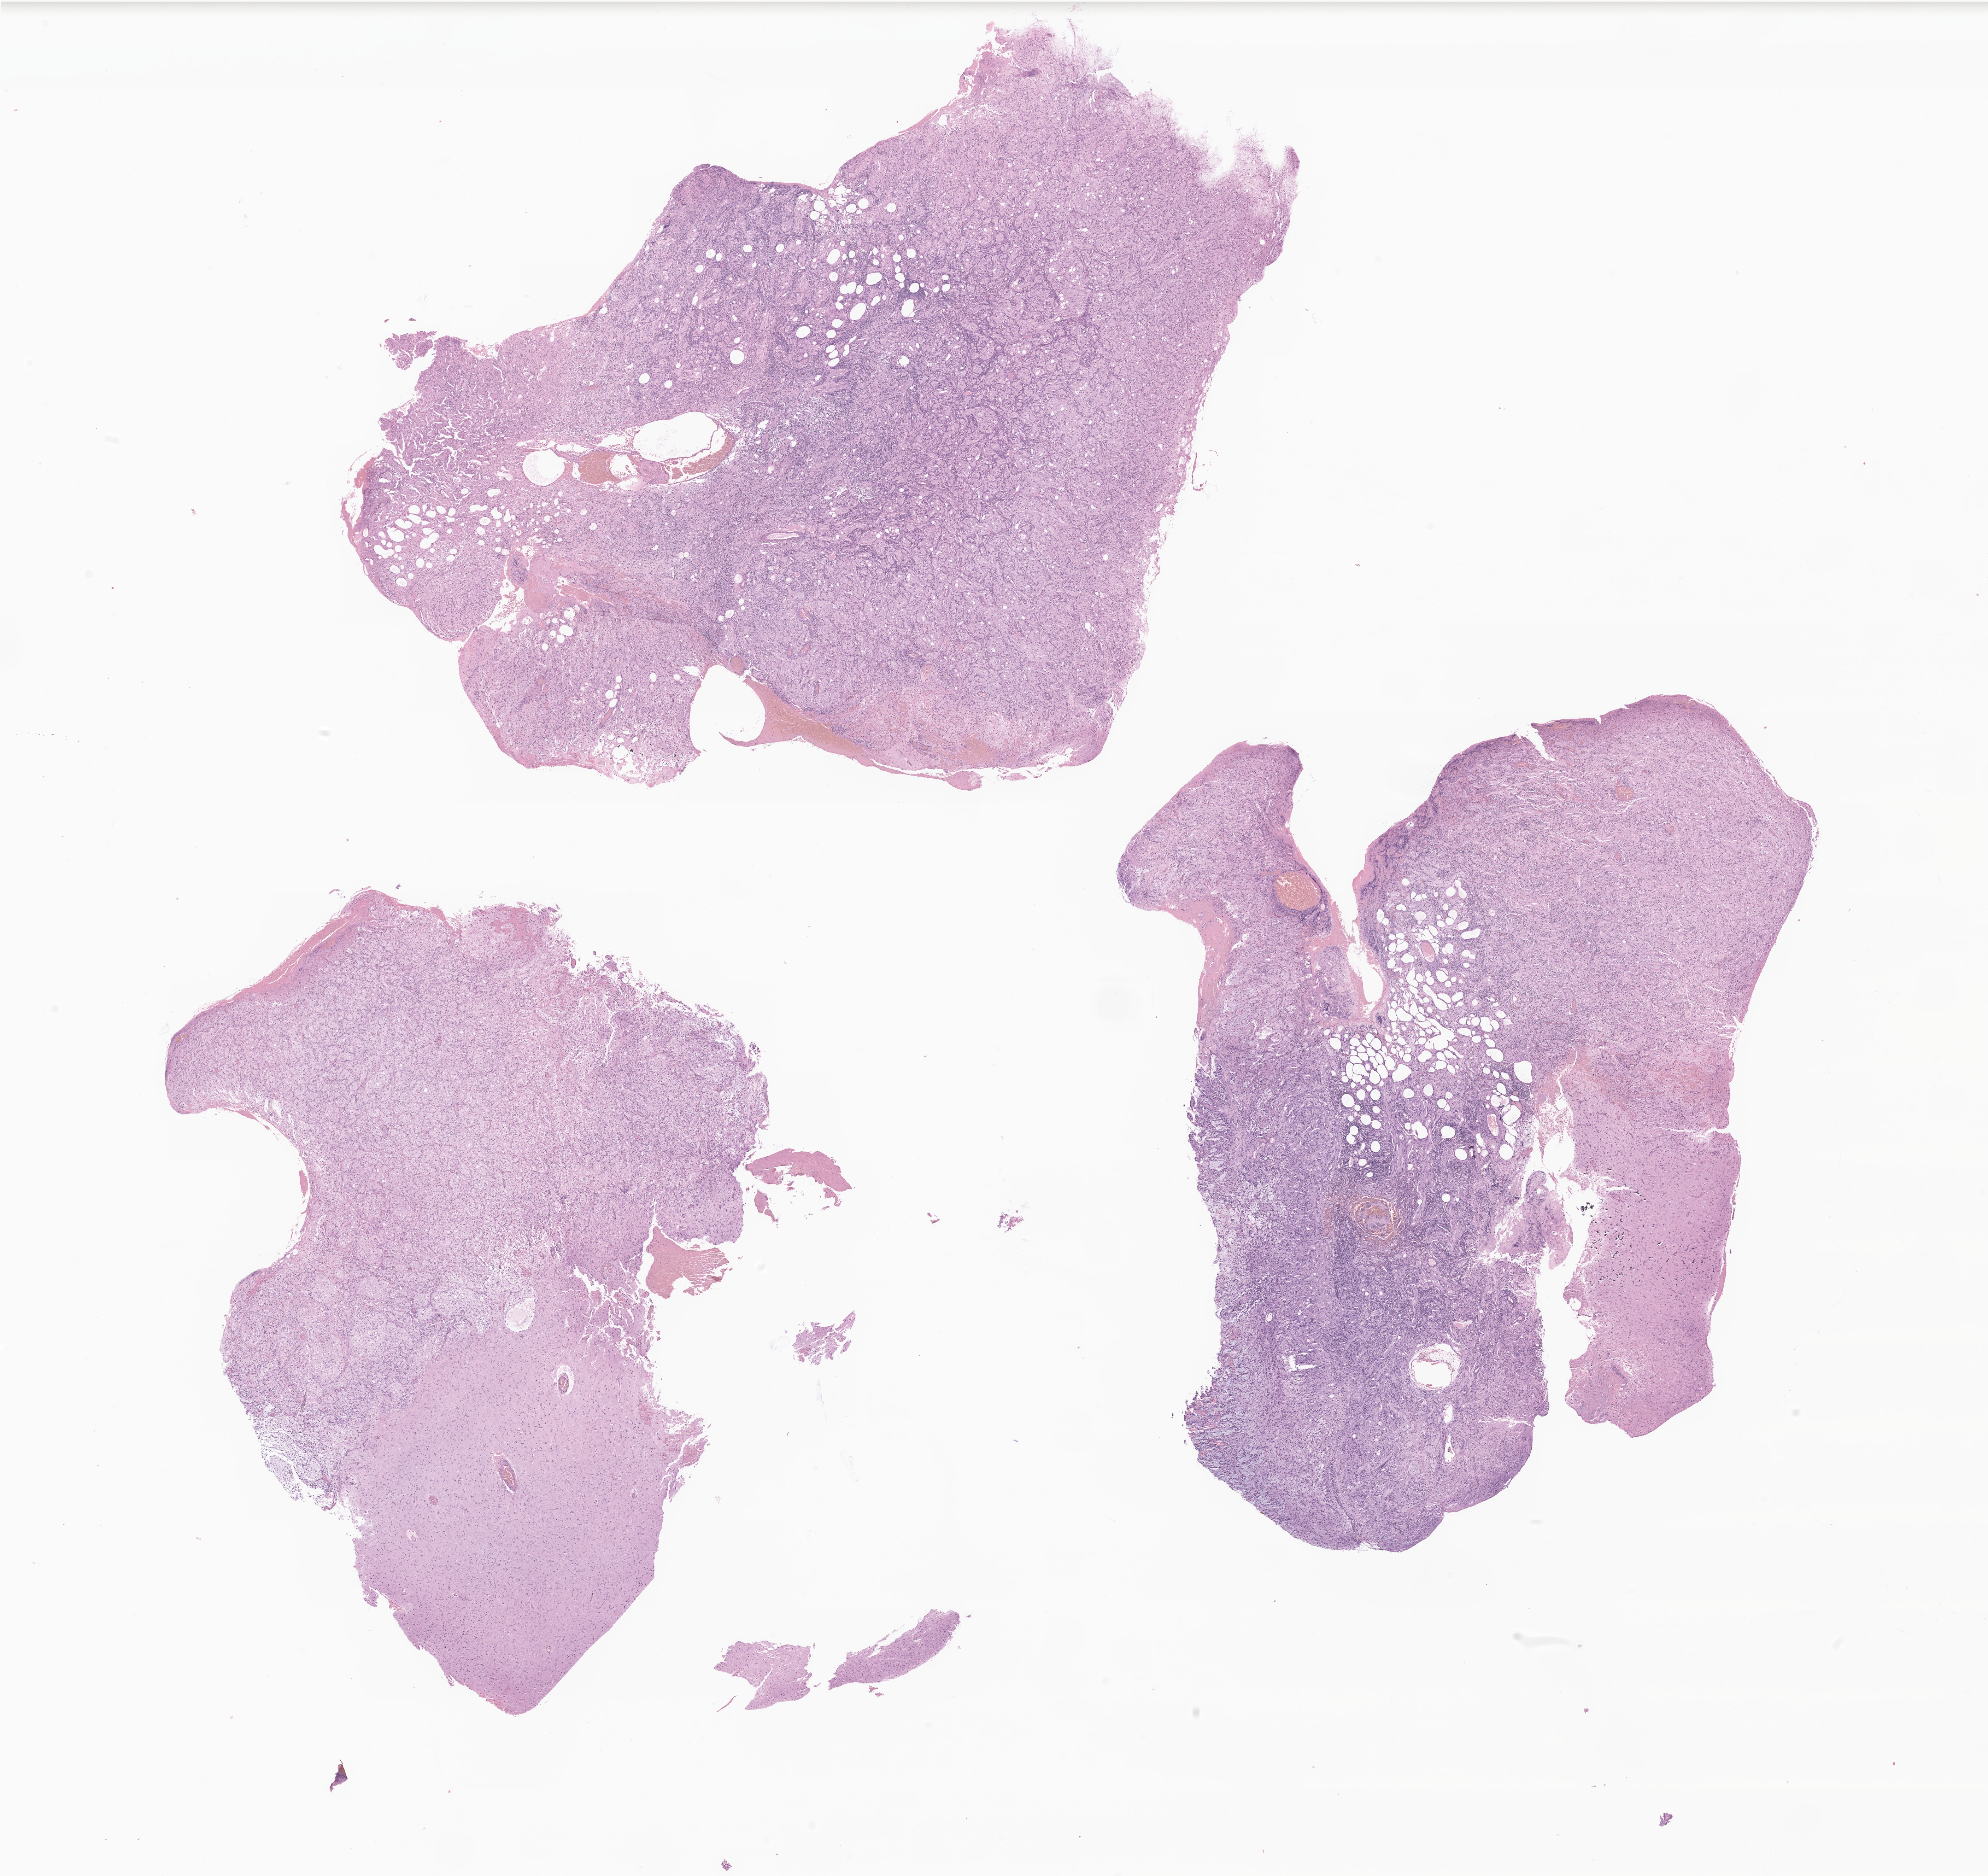
Digitized H&E-stained section of tumor tissue from the brain — a low-resolution overview of the entire scanned area, about 23.7 x 22.4 mm. FFPE section. Female patient, age 214 months (17 years 10 months).
Recorded diagnosis: Astrocytoma, NOS.